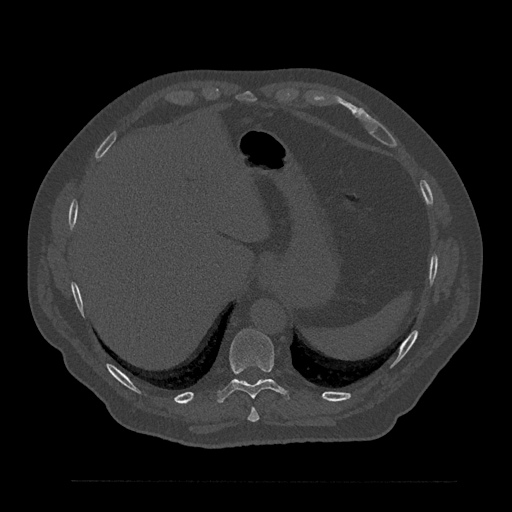
CT including the spine, one axial slice; position 349 of 797 along the scan axis; bone window (W 1800 / L 400 HU); 0.5 mm slice thickness; 512 × 512 image matrix, field of view 430 × 430 mm. Patient: male, 61 years. From the clinical record (not read from this slice): primary cancer: prostate.
Outlined on this slice (semi-automatically segmented with operator editing):
- T10 vertebra: box from (x=216, y=329) to (x=289, y=403) px
- T9 vertebra: (x=248, y=407)–(x=259, y=422)